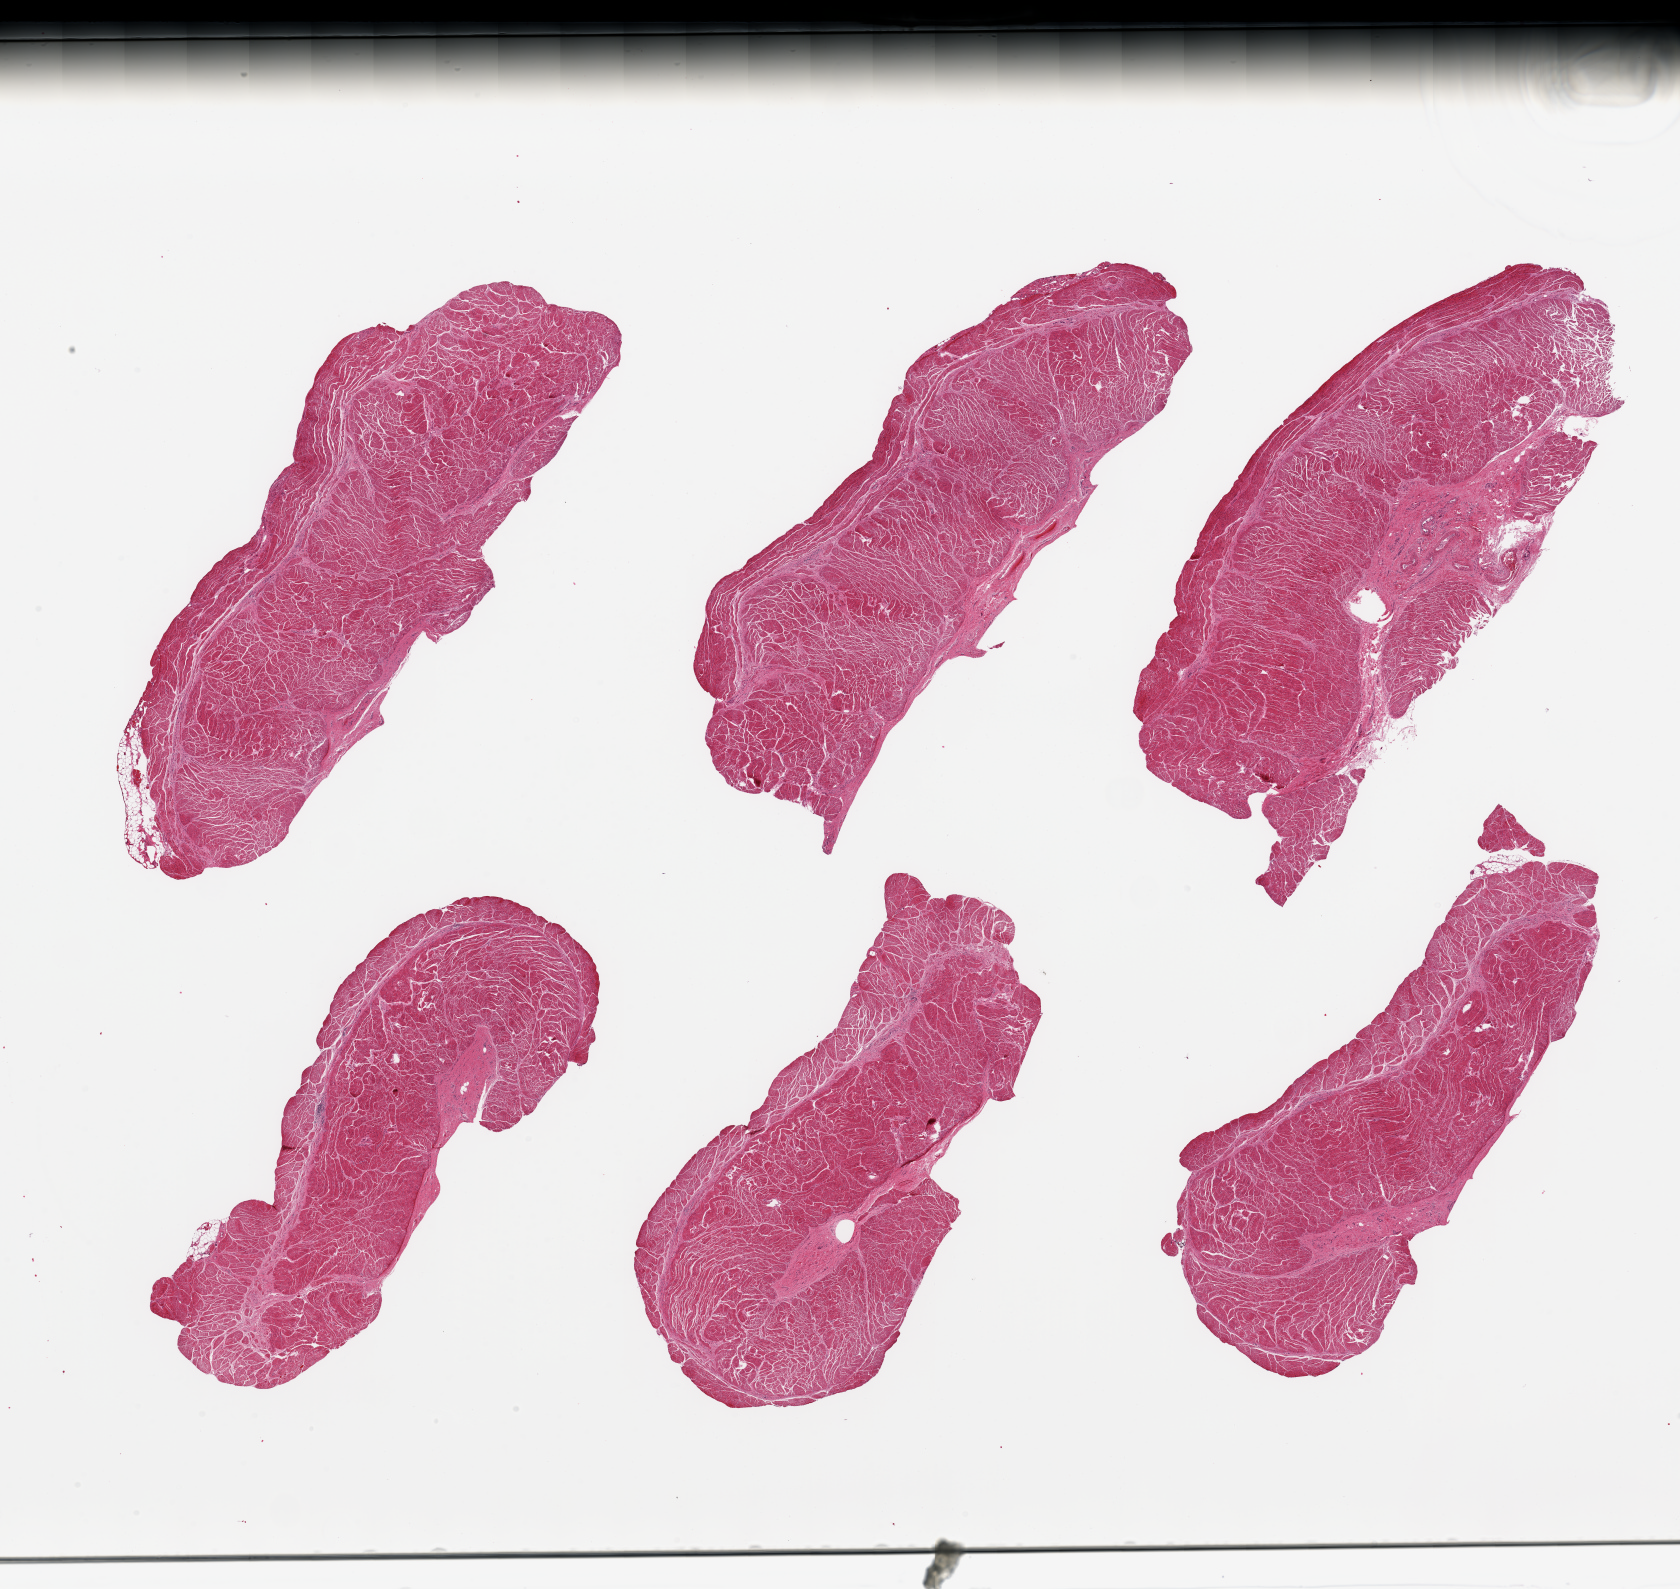
Digitized hematoxylin and eosin (H&E)-stained section — a low-resolution overview of the entire scanned area, about 26.6 x 25.1 mm (from a 20x scan). PAXgene-fixed paraffin-embedded (PFPE) section. Section of esophageal muscle (target tissue). Tissue donor sample. Donor sex: male.
• reviewer comment on this tissue sample: 6 pieces, confirmed target muscularis